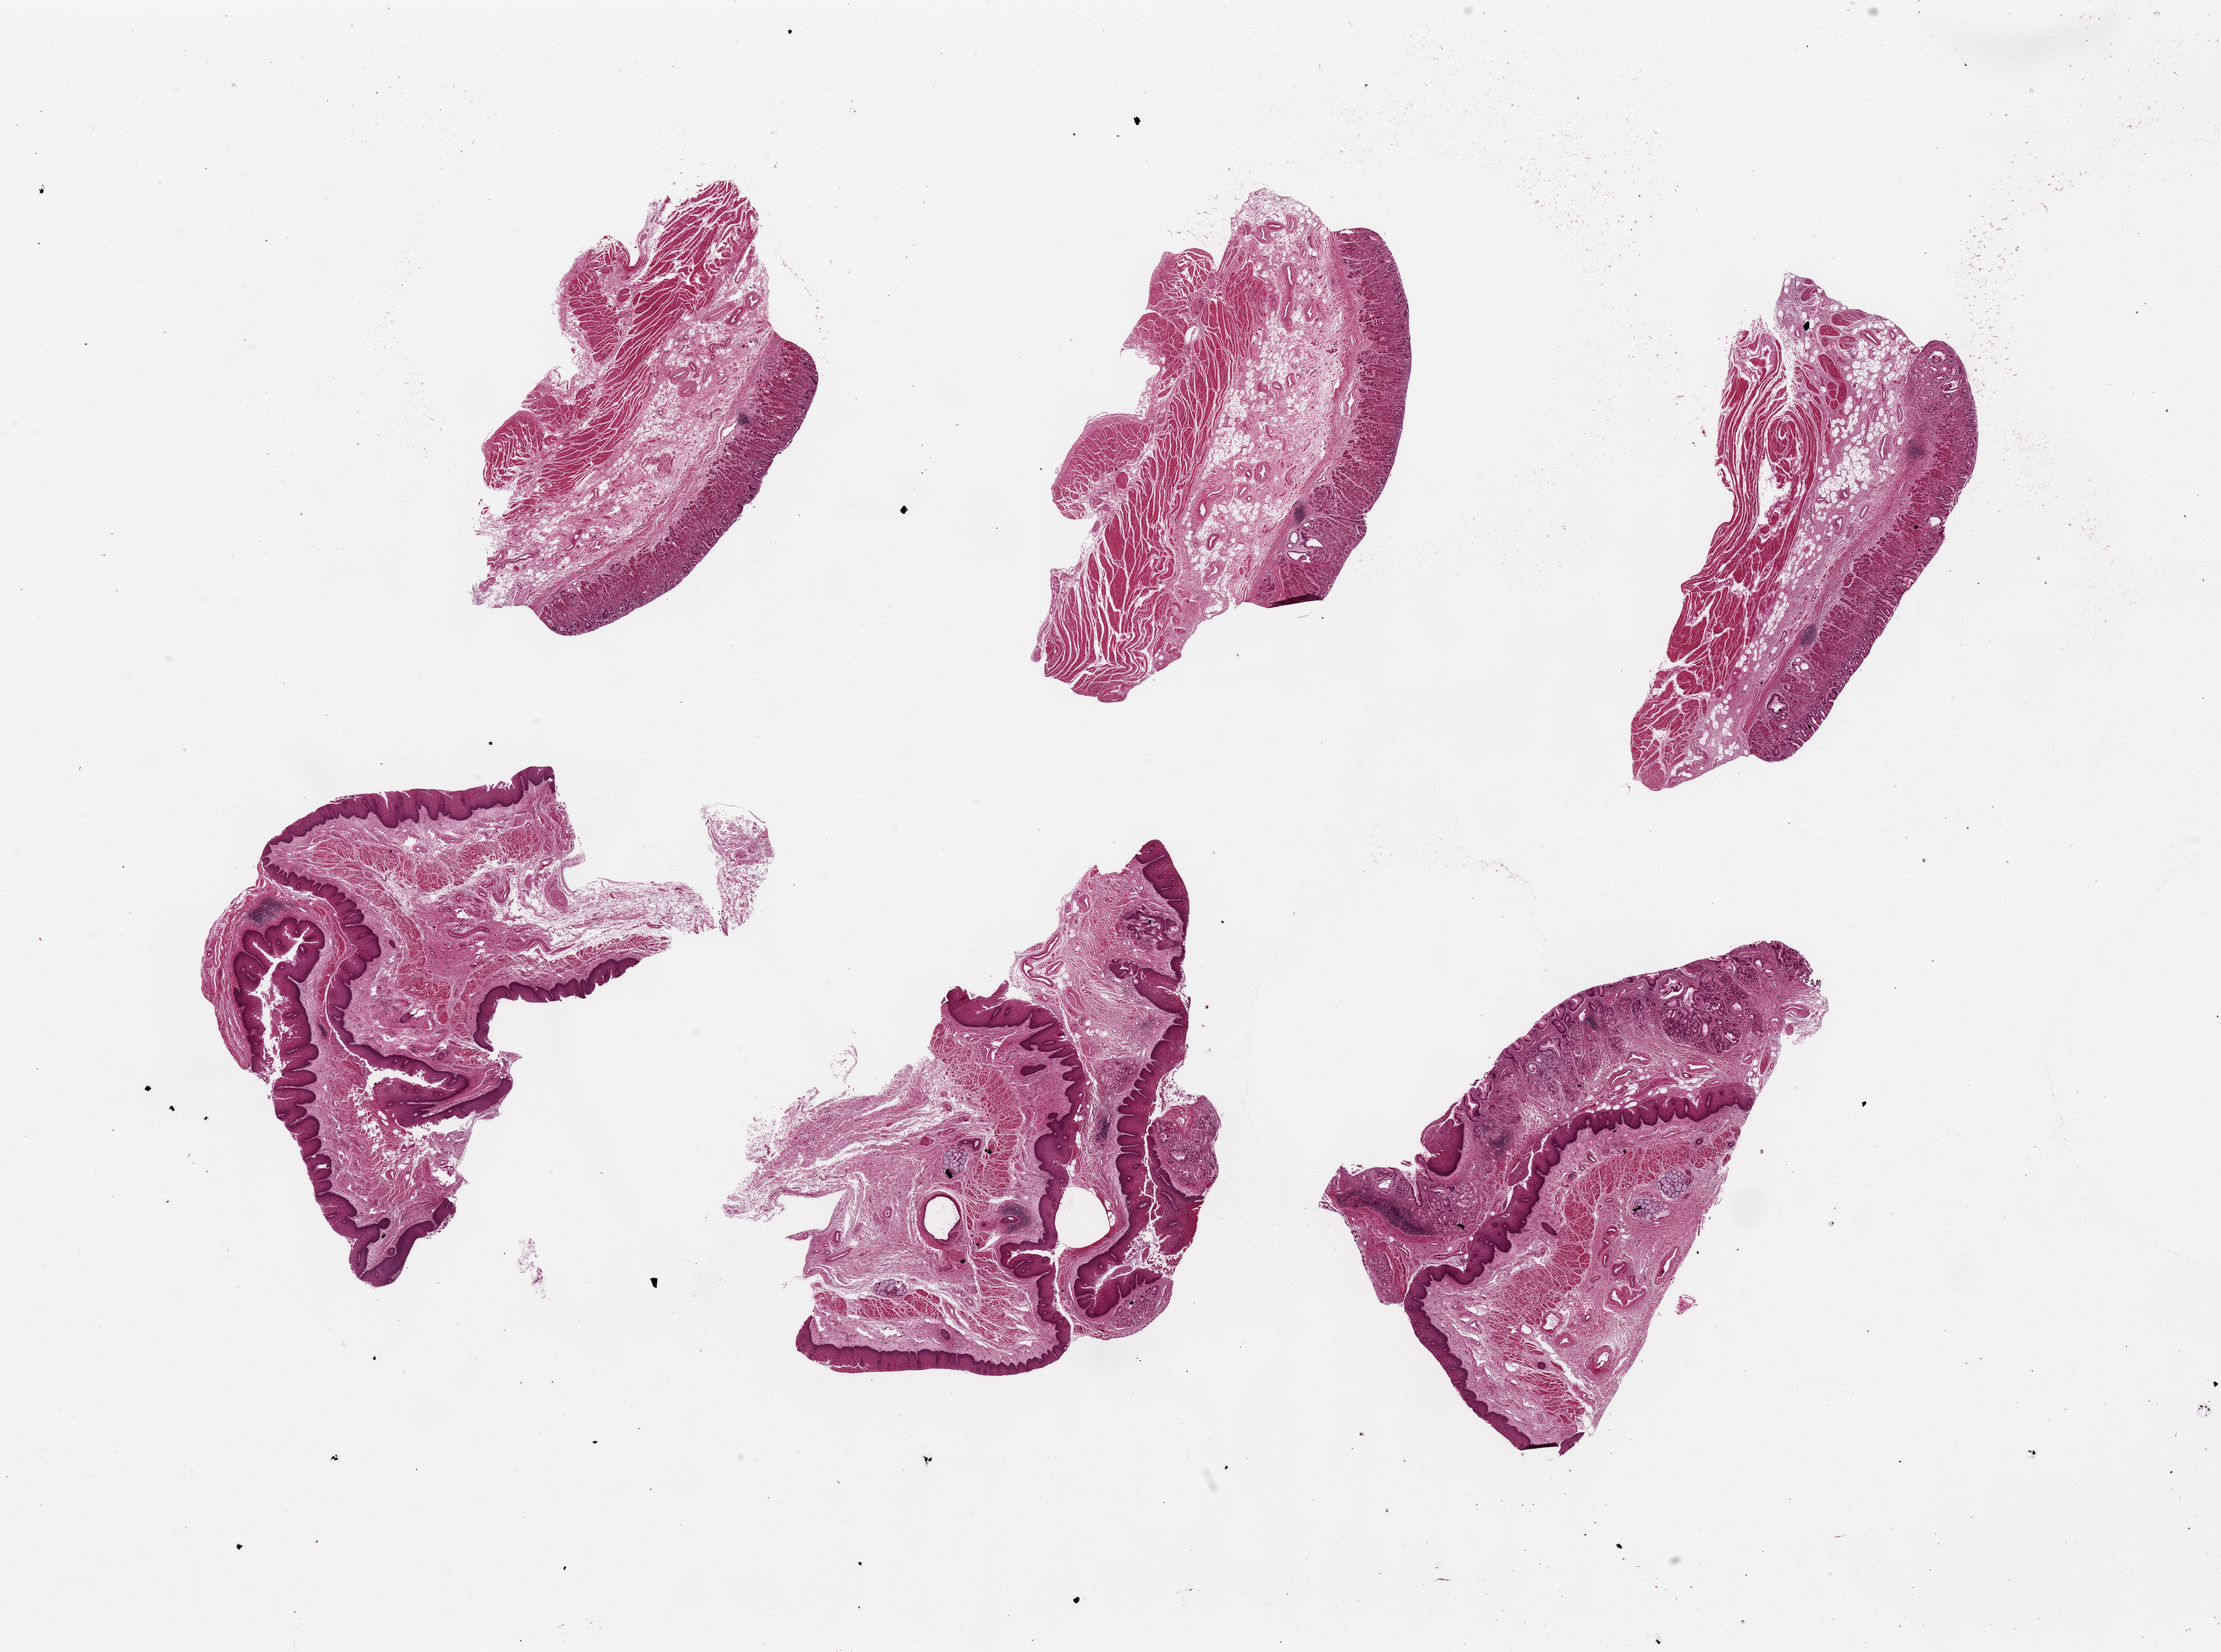
H&E whole-slide image, brightfield, a low-resolution overview of the entire scanned area, about 29.5 x 22.0 mm (acquisition: 20x scan). PAXgene-fixed paraffin-embedded (PFPE) section. Target tissue: stomach. Tissue donor sample. Female donor.
Pathologist's review note for this sample: 6 pieces, up to 8x6mm; 3 pieces with well preserved gastric mucosa and muscle; 3 pieces with squamous and mixed squamous and gastric mucosa without muscularis propria ( on image-see issues).